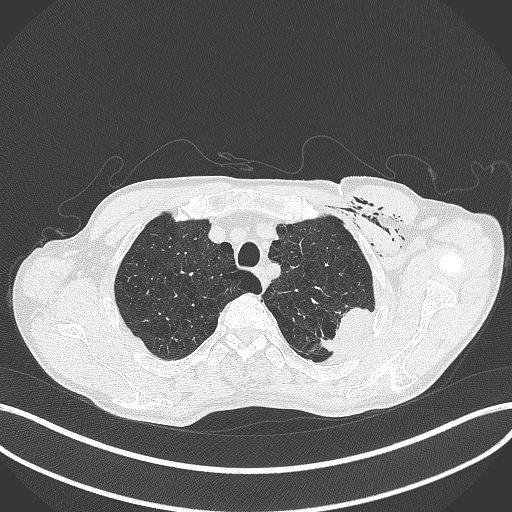
Chest CT, one axial slice. Position 349 of 457 along the scan axis. Reconstruction kernel B70f. 120 kVp. Lung window (W 1500 / L -600 HU). 512 × 512 image matrix, field of view 400 × 400 mm. Male patient, age 58 years. Case-level facts recorded for this patient, not image findings: clinical TNM (as recorded): T3 N0 M0.
Annotated regions visible in this slice (bounding box drawn by a radiologist):
- lung tumour (recorded histology: adenocarcinoma): bounding box <319,299,374,359> (left, top, right, bottom; pixels)